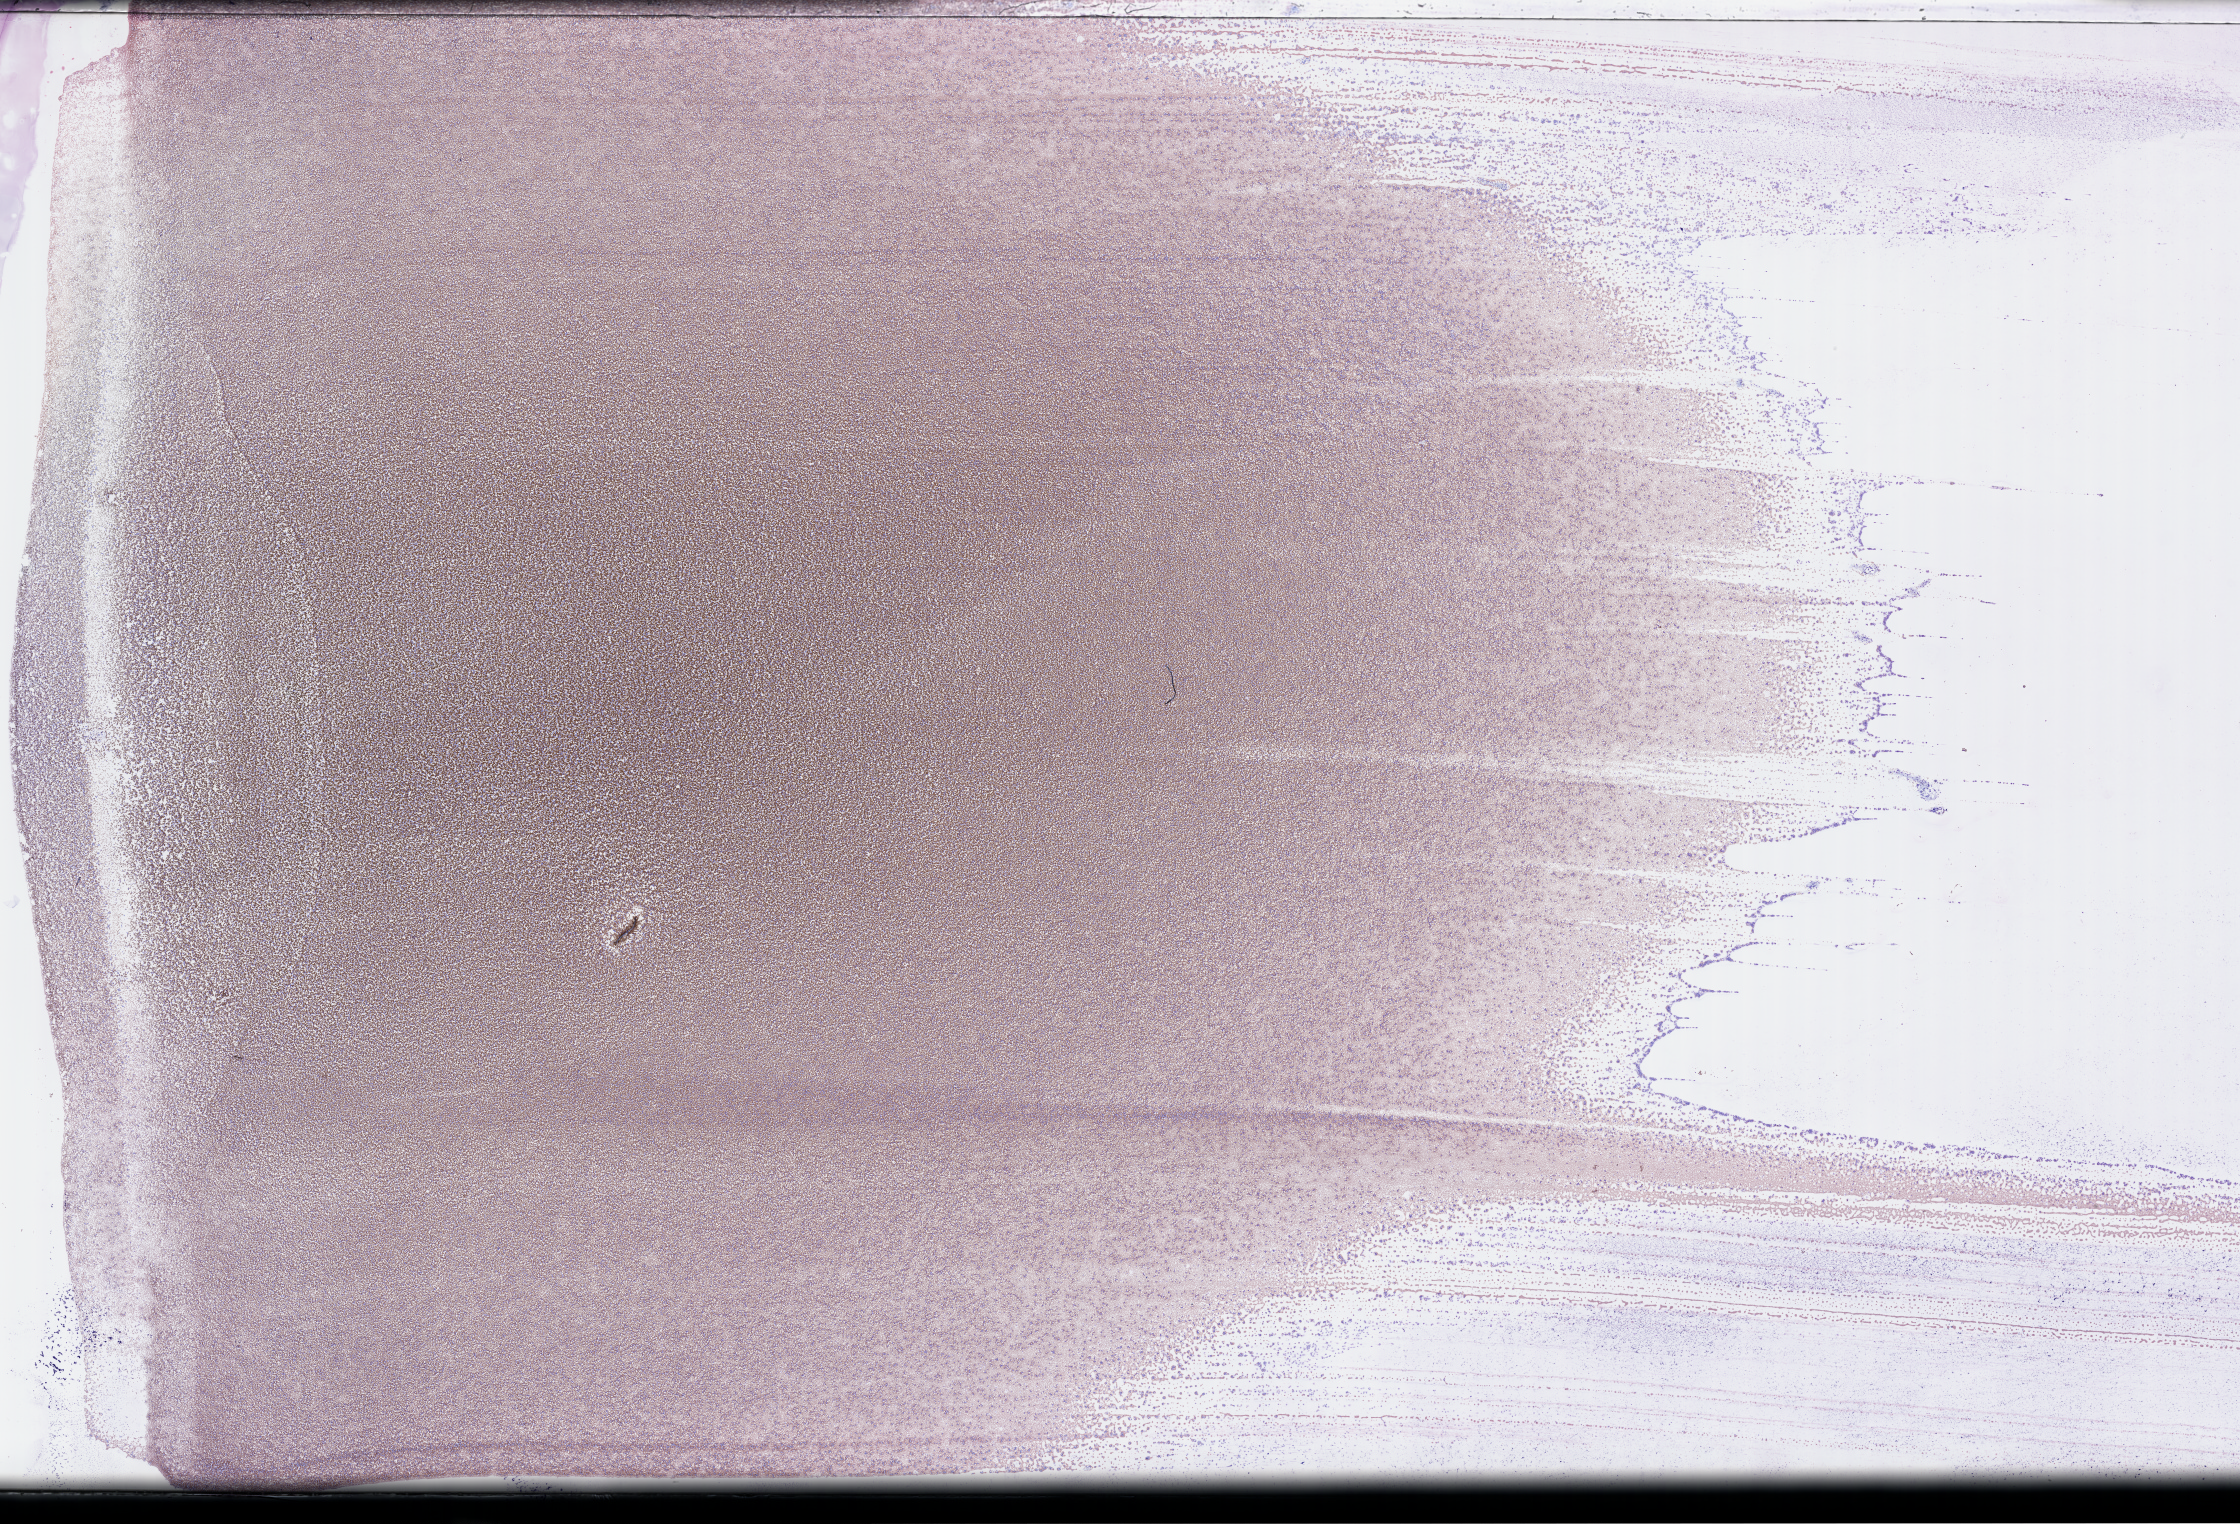
Whole-slide image of a whole blood smear, Wright–Giemsa stain, low-resolution overview of the scanned area, about 36.2 x 24.6 mm, smear from an EDTA sample, specimen time point: collected at baseline (before treatment). Female patient.
* patient diagnosis: Acute Myeloid Leukemia Not Otherwise Specified